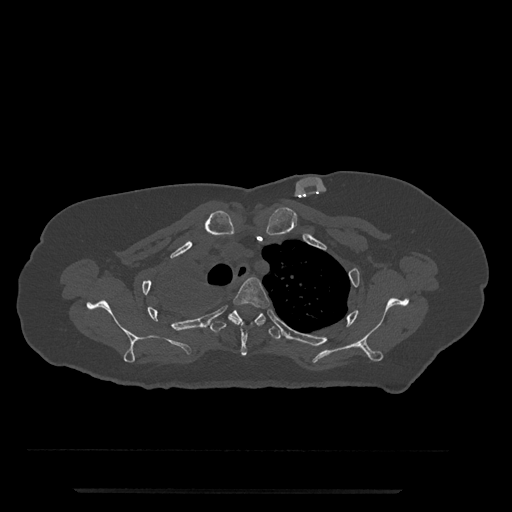
CT including the spine, one axial slice; slice 615 of 797 in the series (ordered by position); 120 kVp; bone window (W 1800 / L 400 HU); 0.5 mm slice thickness; 512 × 512 image matrix, field of view 440 × 440 mm. Patient: female, 51 years. From the clinical record (not read from this slice): primary cancer: neuro; vertebrae with lytic lesions (as recorded): T8.
Outlined on this slice (semi-automatic segmentation, software-assisted and operator-edited):
- T3 vertebra: bounding box [x1, y1, x2, y2] px = [233, 277, 270, 356]
- T4 vertebra: [210, 310, 281, 340]